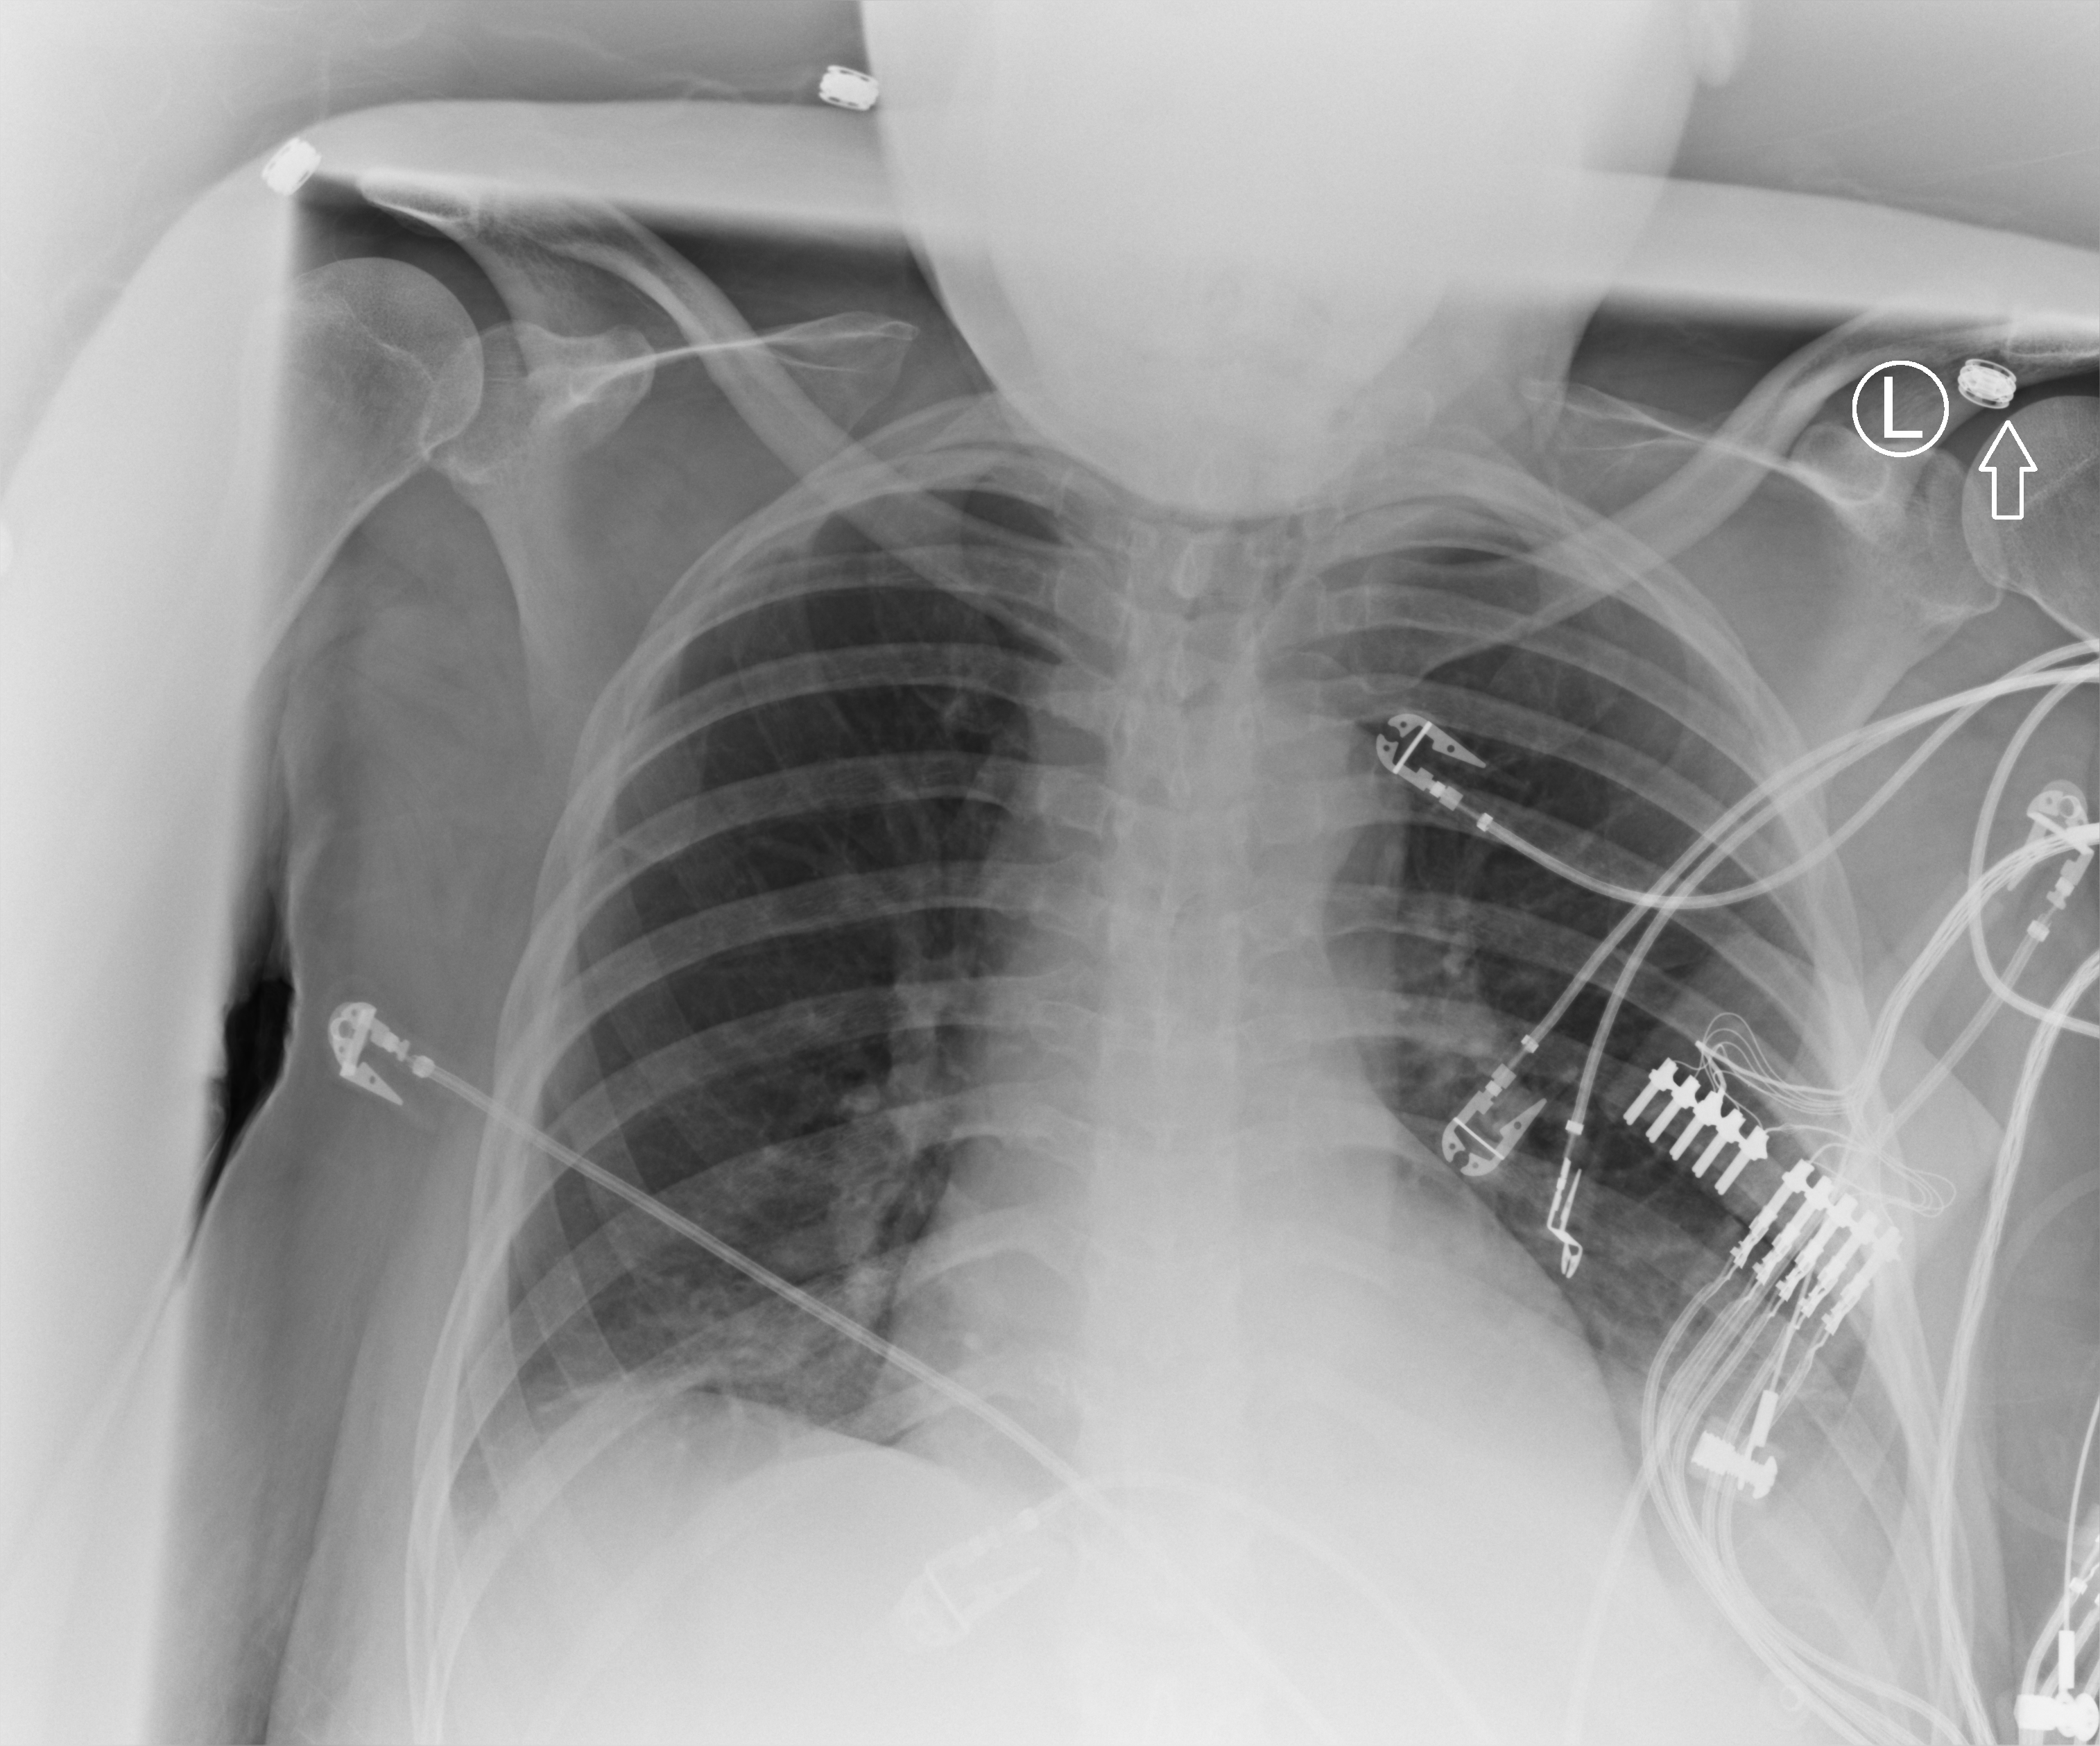
Bedside chest radiograph (computed radiography). Female patient hospitalised with COVID-19, age 18–59 years.
From the hospital-stay record, not from the radiograph (when in the stay this image was taken is not recorded): mechanically ventilated during this hospital stay: no.